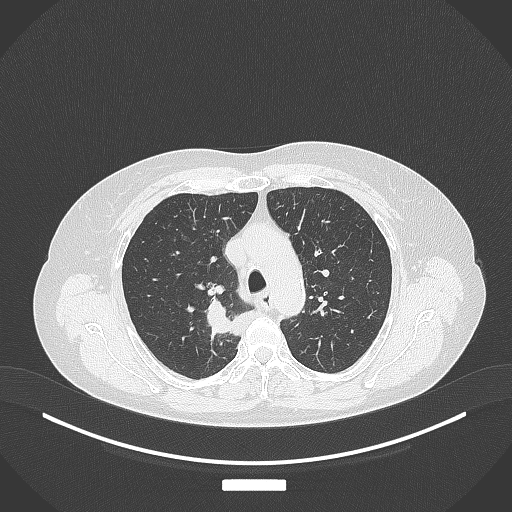
Chest CT, one axial slice. Position 279 of 357 along the scan axis. Lung window (W 1500 / L -600 HU). 512 × 512 image matrix. Female patient, age 62 years. Case-level facts recorded for this patient, not image findings: clinical TNM (as recorded): T1c N1 M0.
Structures marked on this image (rectangle marked by the reading radiologist):
- lung tumour (recorded histology: squamous cell carcinoma): bounding box <203,296,232,333> (left, top, right, bottom; pixels)